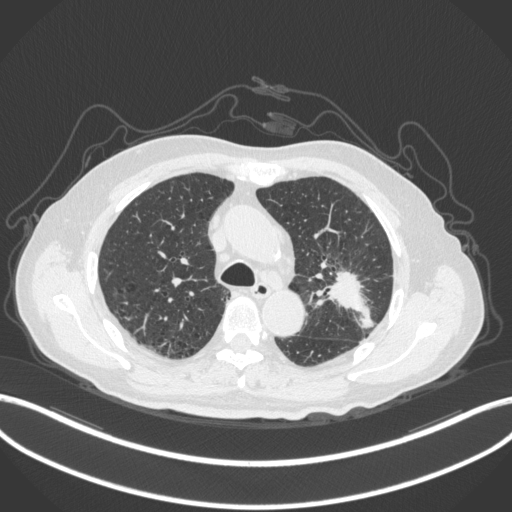
Chest CT, one axial slice; position 199 of 331 along the scan axis; reconstruction kernel B31f; 120 kVp; lung window (W 1500 / L -600 HU); 1 mm slice thickness; 512 × 512 image matrix. Male patient, age 79 years. From the clinical record (not read from this slice): clinical TNM (as recorded): T2a N1 M1.
Outlined on this slice (rectangle marked by the reading radiologist):
- lung tumour (recorded histology: adenocarcinoma): box from (x=325, y=264) to (x=373, y=328) px